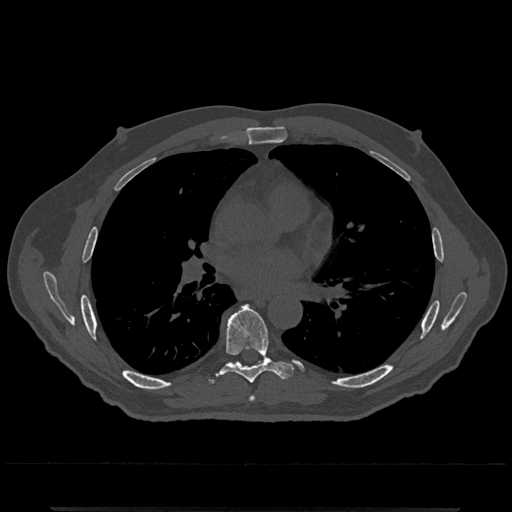
CT including the spine, one axial slice; slice 721 of 797 in the series (ordered by position); 120 kVp; bone window (W 1800 / L 400 HU); 0.5 mm slice thickness; 512 × 512 image matrix. Patient: male, 67 years. Case-level facts recorded for this patient, not image findings: primary cancer: prostate.
Structures marked on this image (semi-automatically segmented with operator editing):
- T6 vertebra: bounding box <249,396,256,402> (left, top, right, bottom; pixels)
- T7 vertebra: <220,305,292,384>